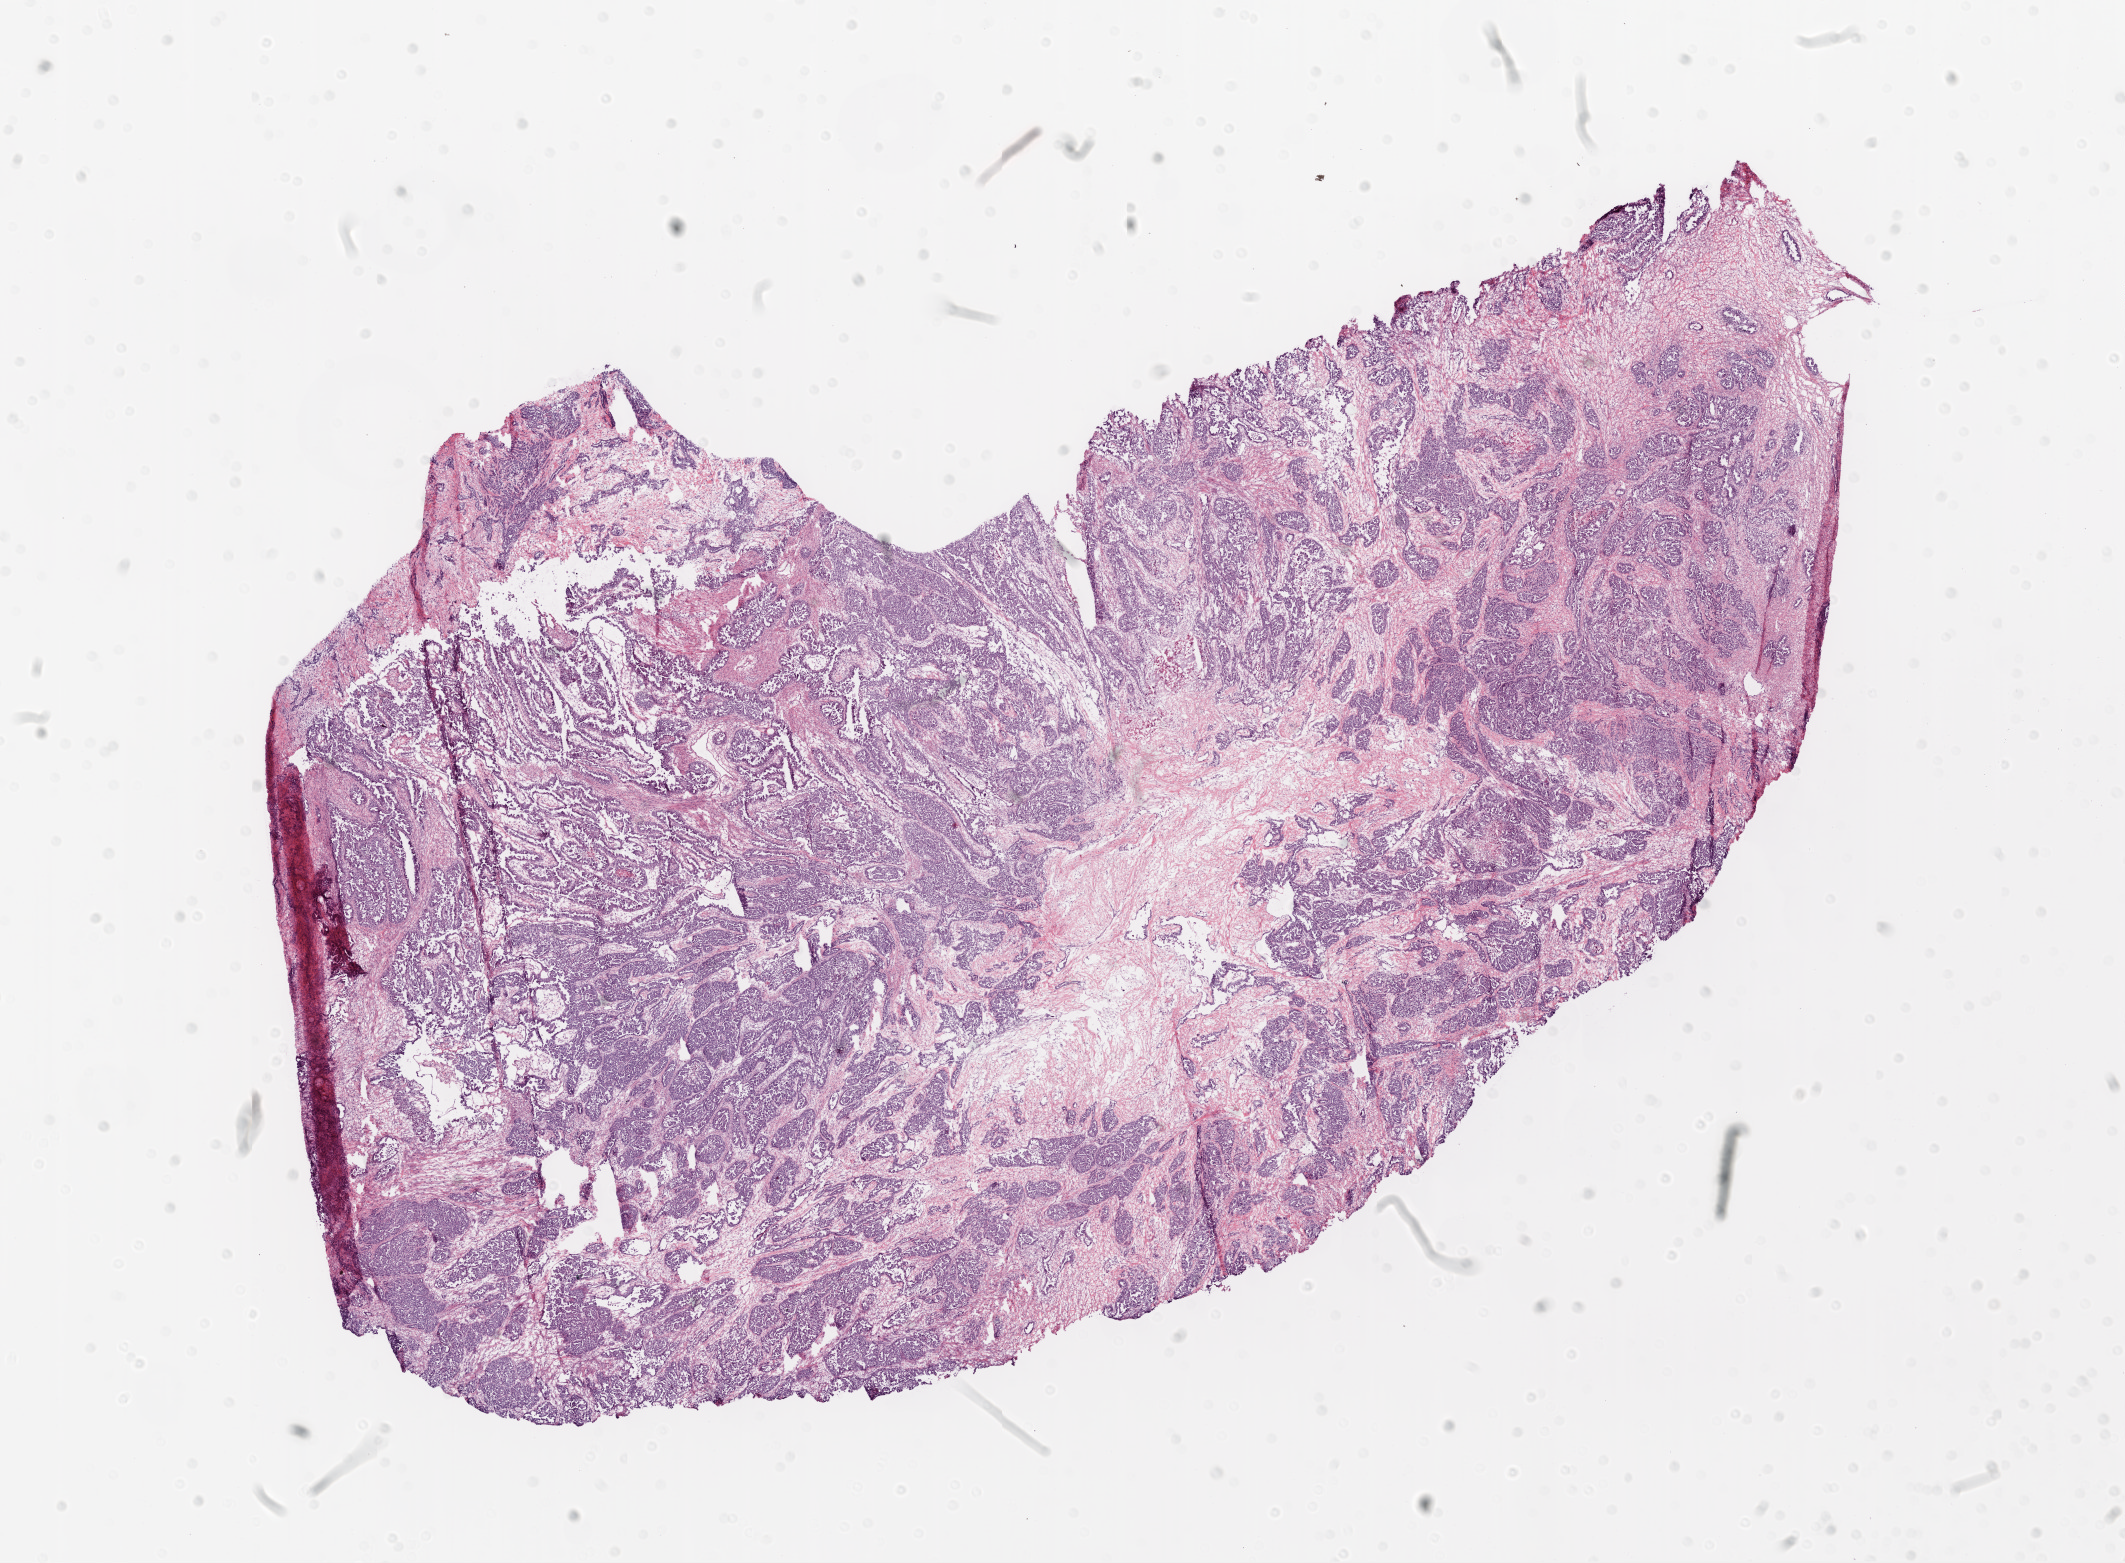
Digitized H&E tissue section (whole slide), shown as a low-resolution overview of the whole scanned area (about 17.1 x 12.5 mm). Frozen section from the bottom of the tissue portion. Primary tumour sample from the ovary. Female patient; age at initial diagnosis 56 years. Histologic grade: G3 (poorly differentiated). Slide review estimates, as recorded: tumour cells 70%, tumour nuclei 95%, normal cells 0%, stromal cells 30%, necrosis 0%.
FIGO stage: IIIC. Diagnosis: Serous cystadenocarcinoma, NOS.